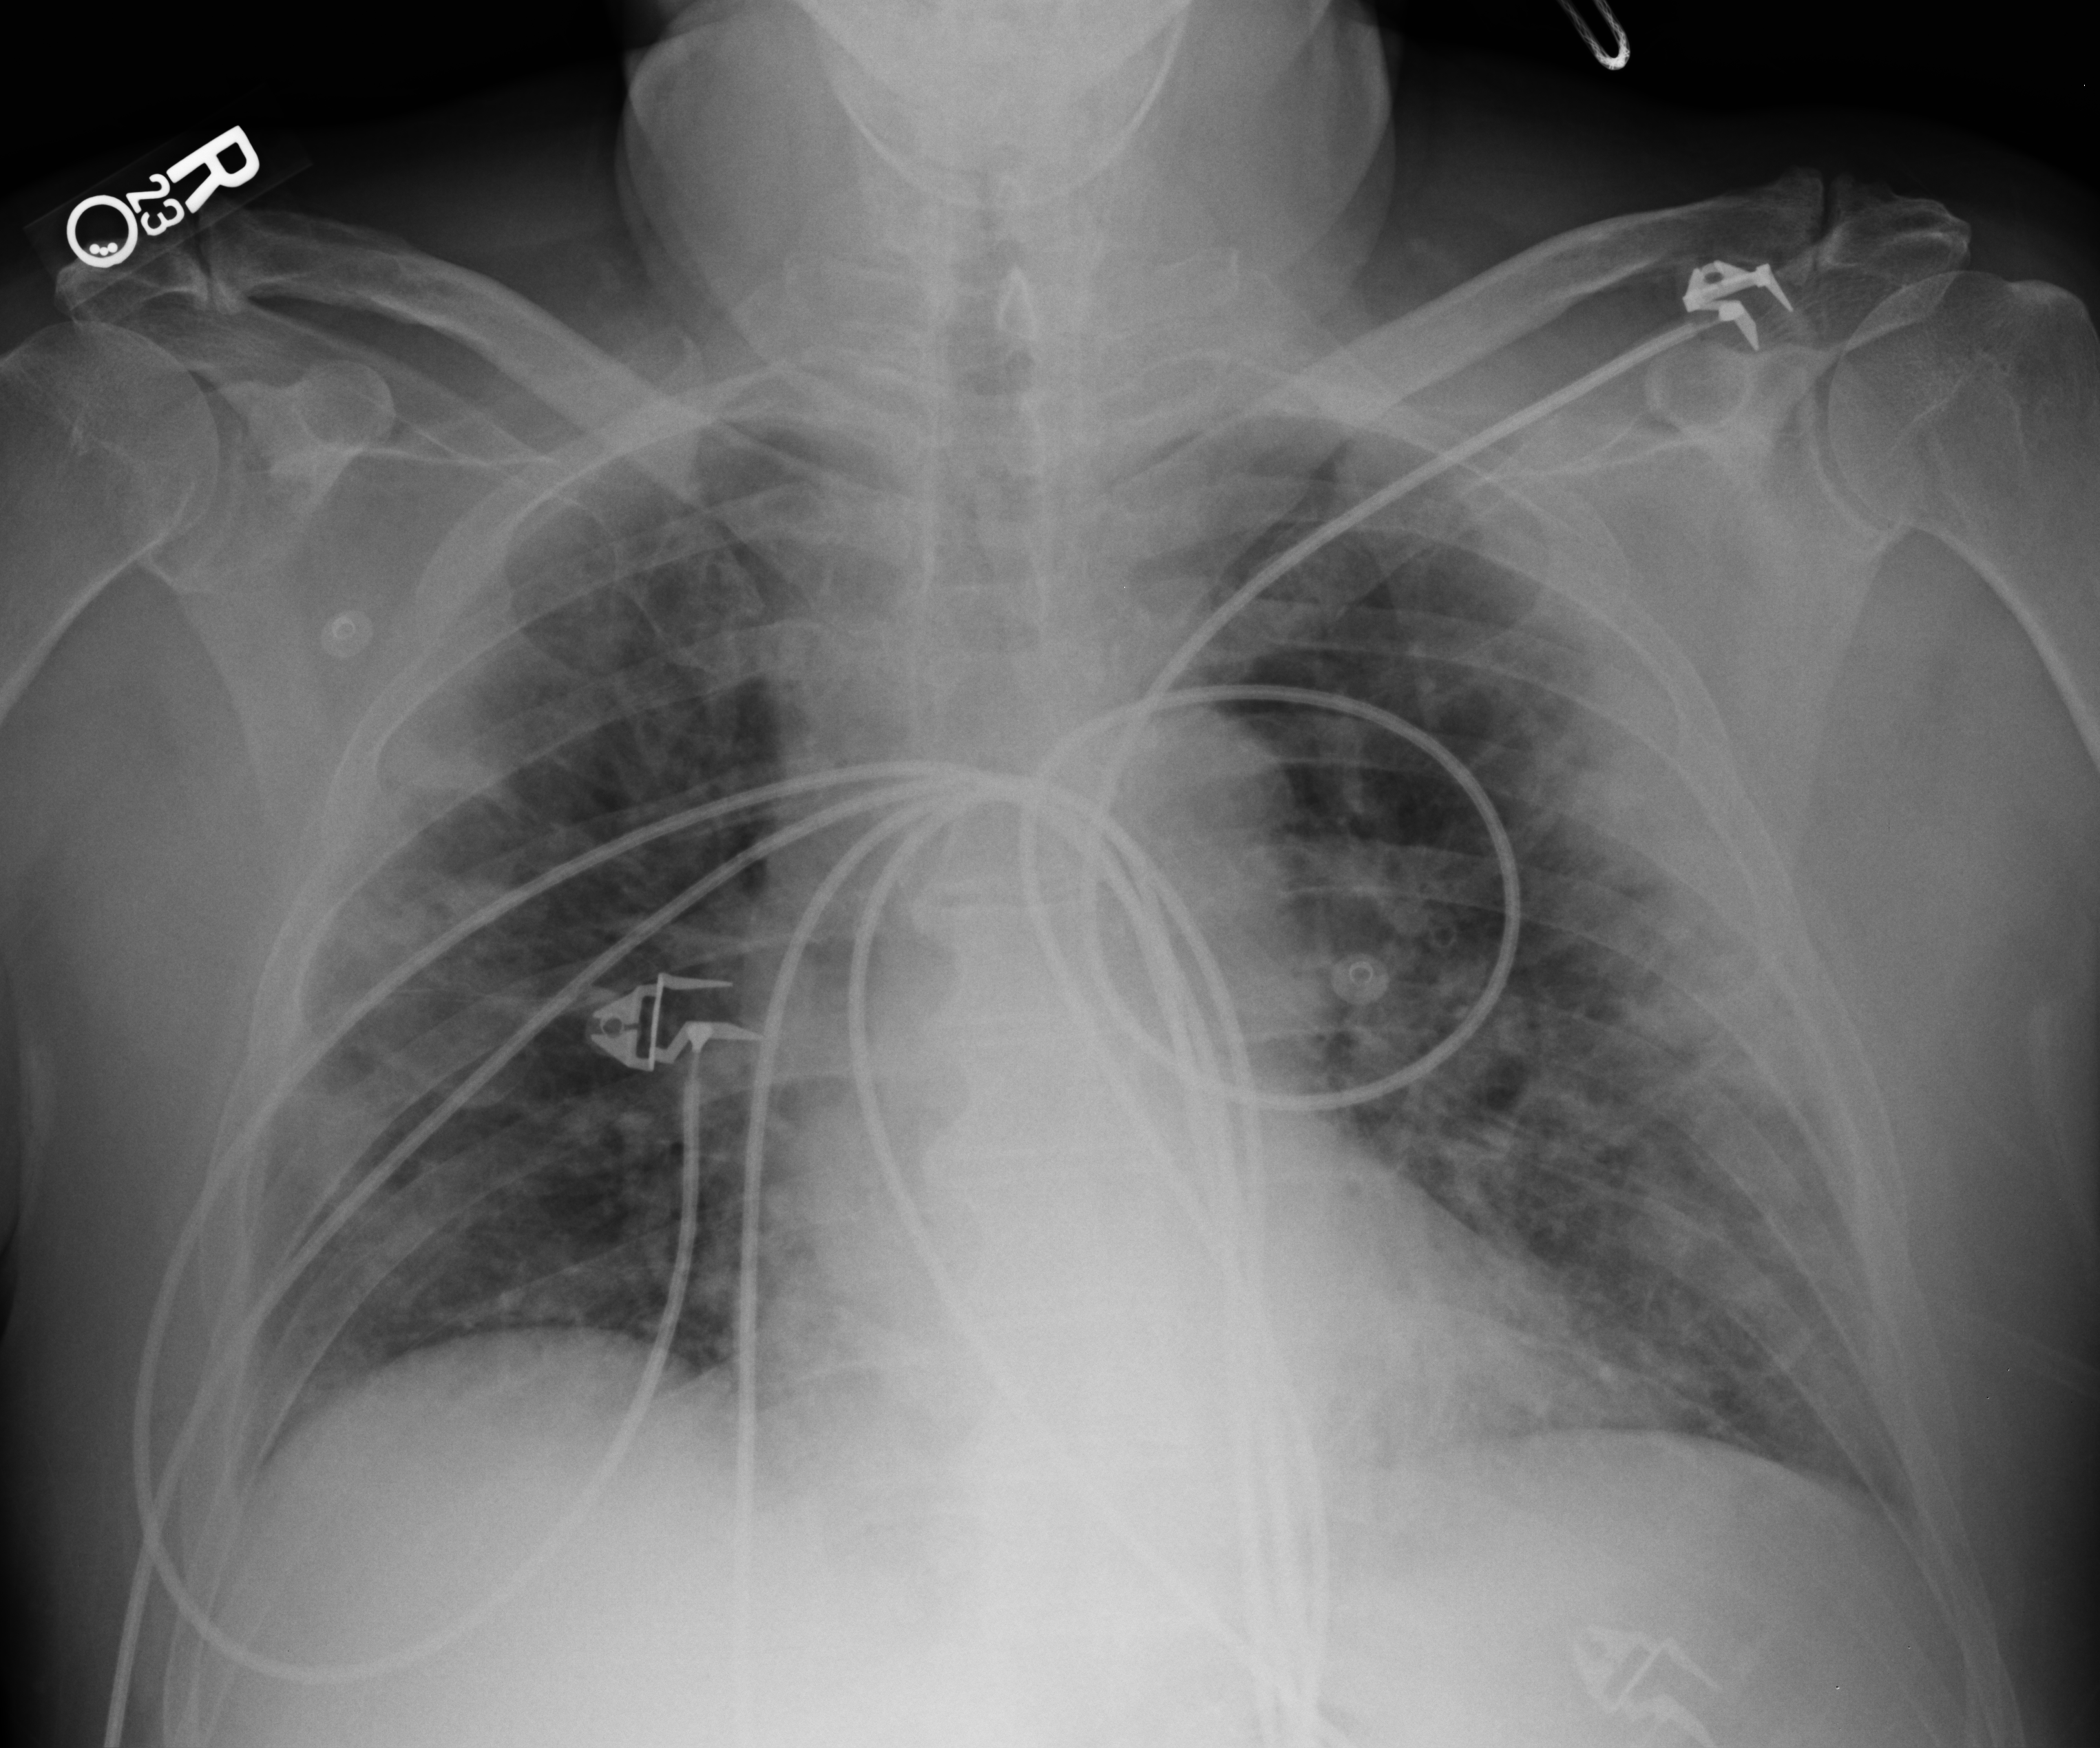
Chest X-ray (portable), anteroposterior (AP) projection. Patient hospitalised with COVID-19; male, aged 60–74 years.
From the hospital-stay record, not from the radiograph (when in the stay this image was taken is not recorded): length of hospital stay: 13 days; mechanically ventilated during this hospital stay: no; admitted to intensive care during this hospital stay: no.